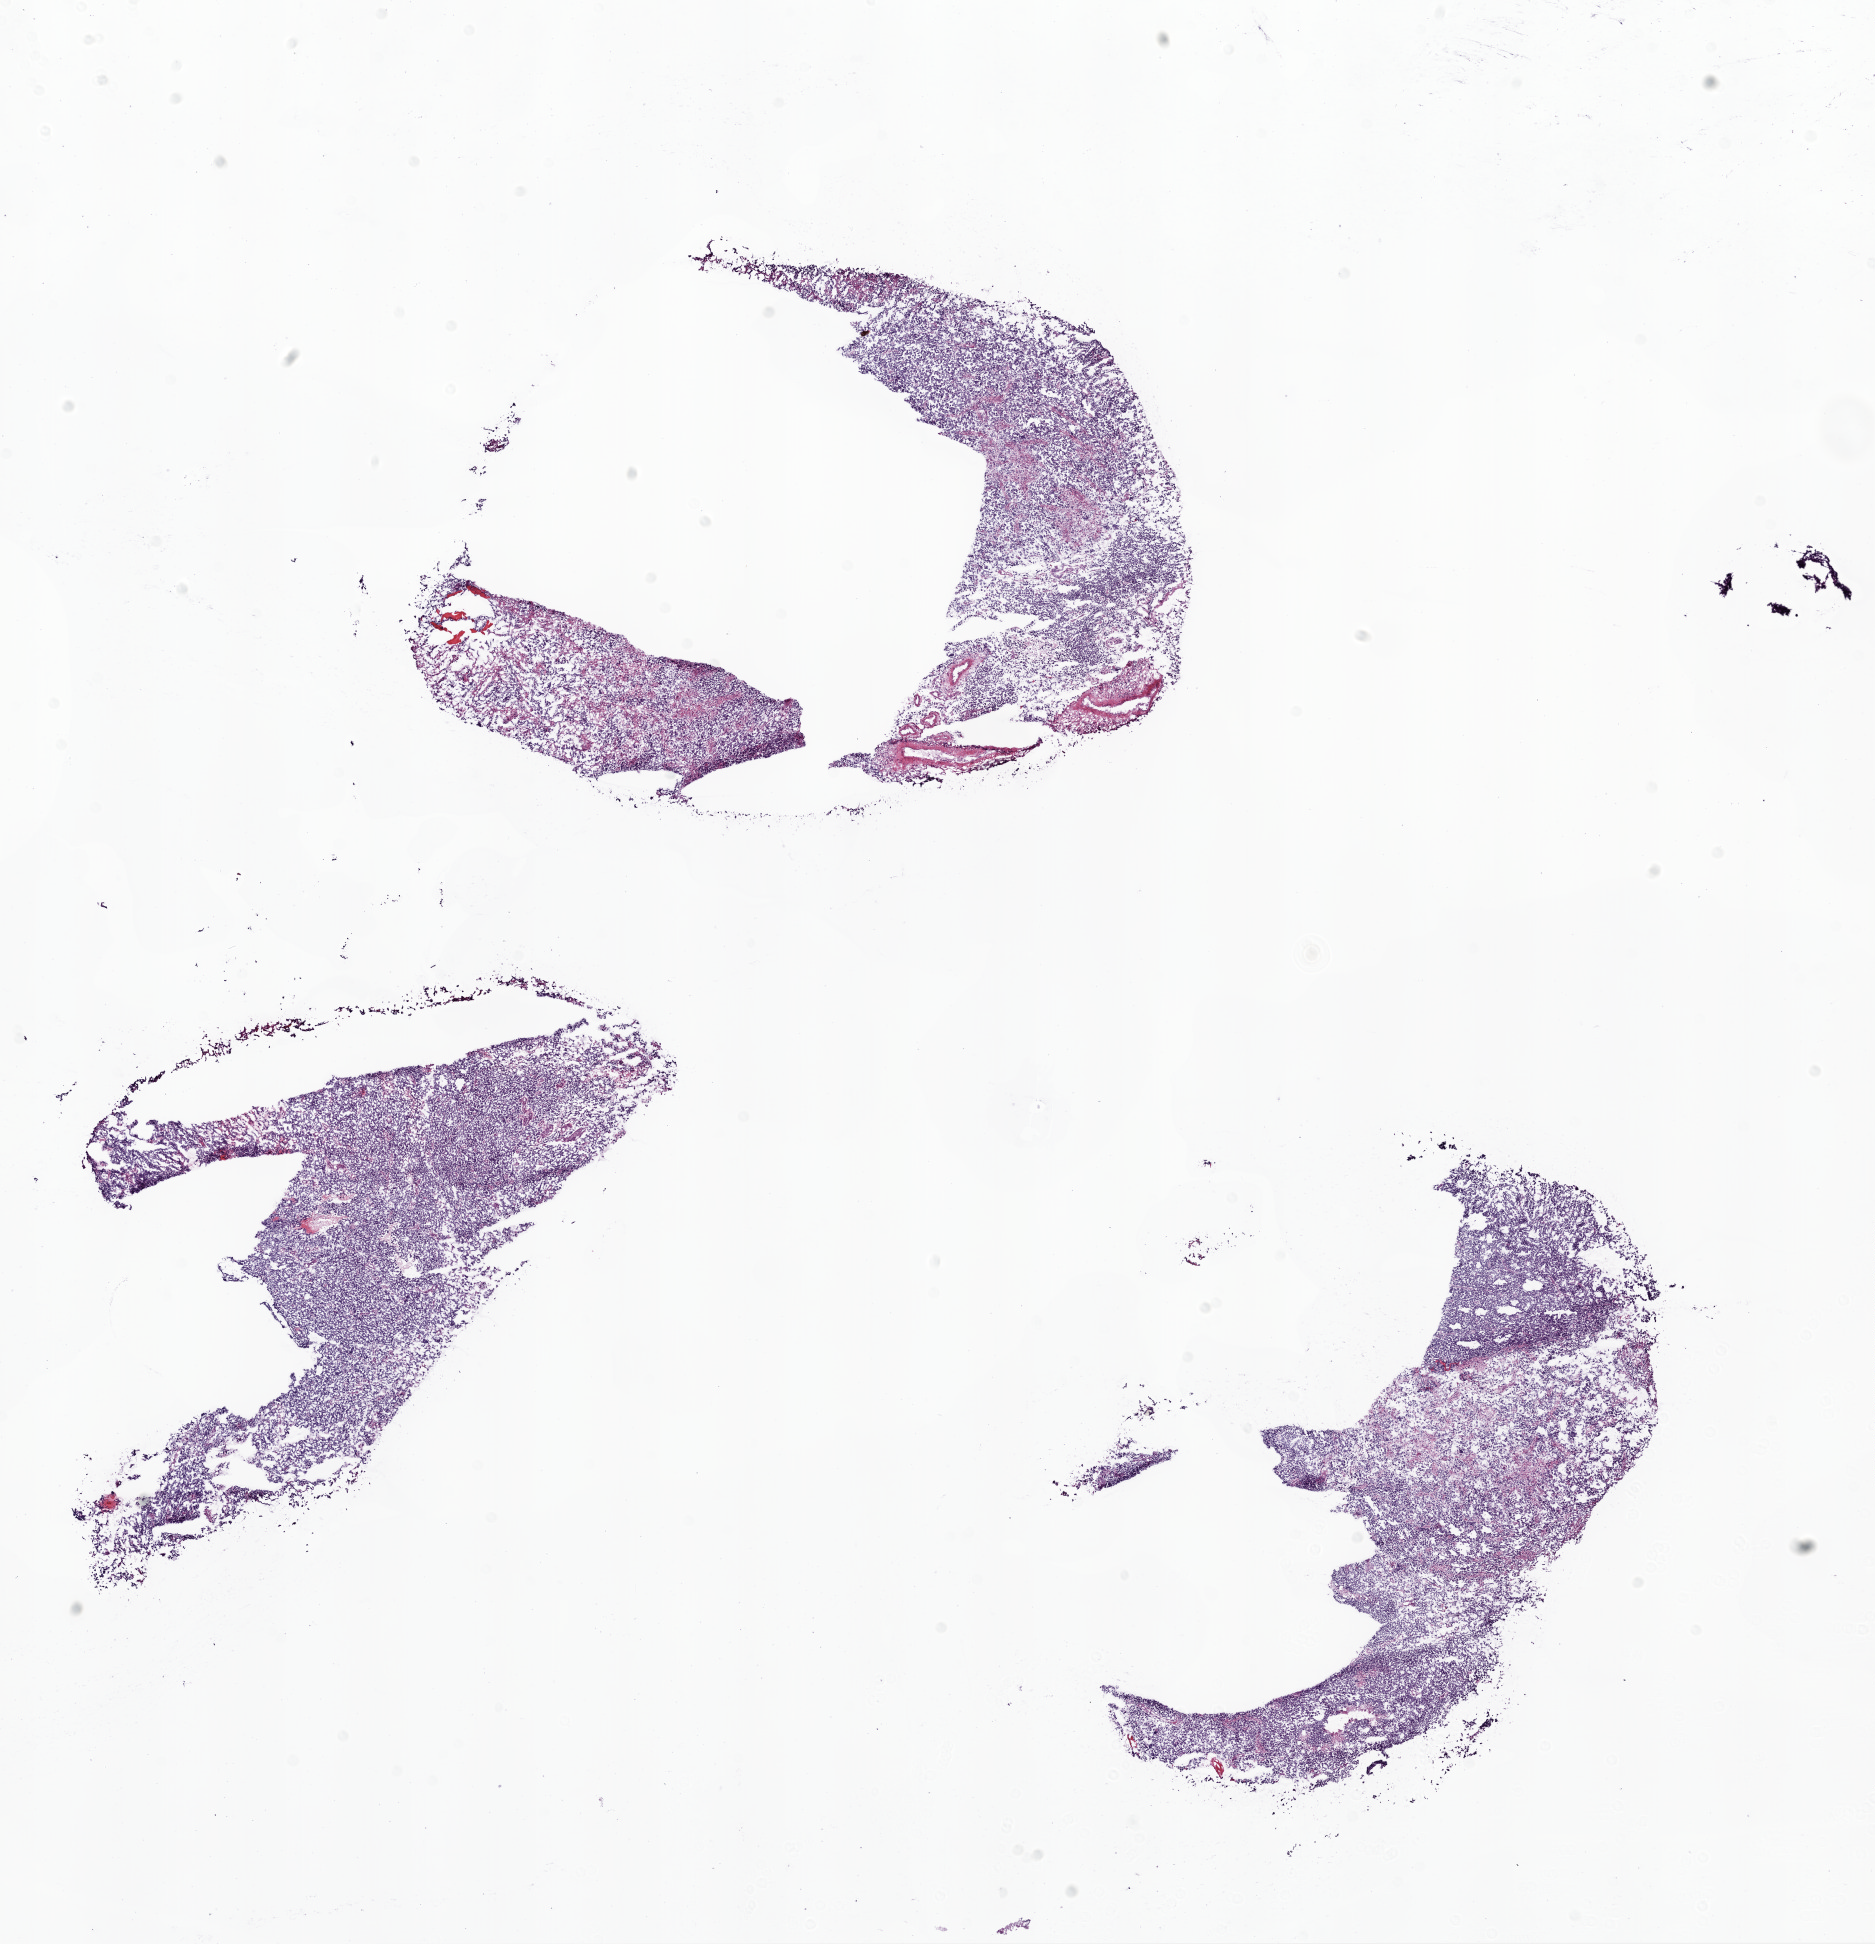
Whole-slide histology image, Hematoxylin and eosin (H&E) stained, a low-resolution overview of the entire scanned area, about 15.0 x 15.6 mm, frozen section, sample: primary tumour, brain. Male patient; age at initial diagnosis 31 years. Pathologist review of this section (percent, as recorded): tumour cells 95%, tumour nuclei 95%, normal cells 0%, stromal cells 3%, necrosis 2%.
• diagnosis: Glioblastoma